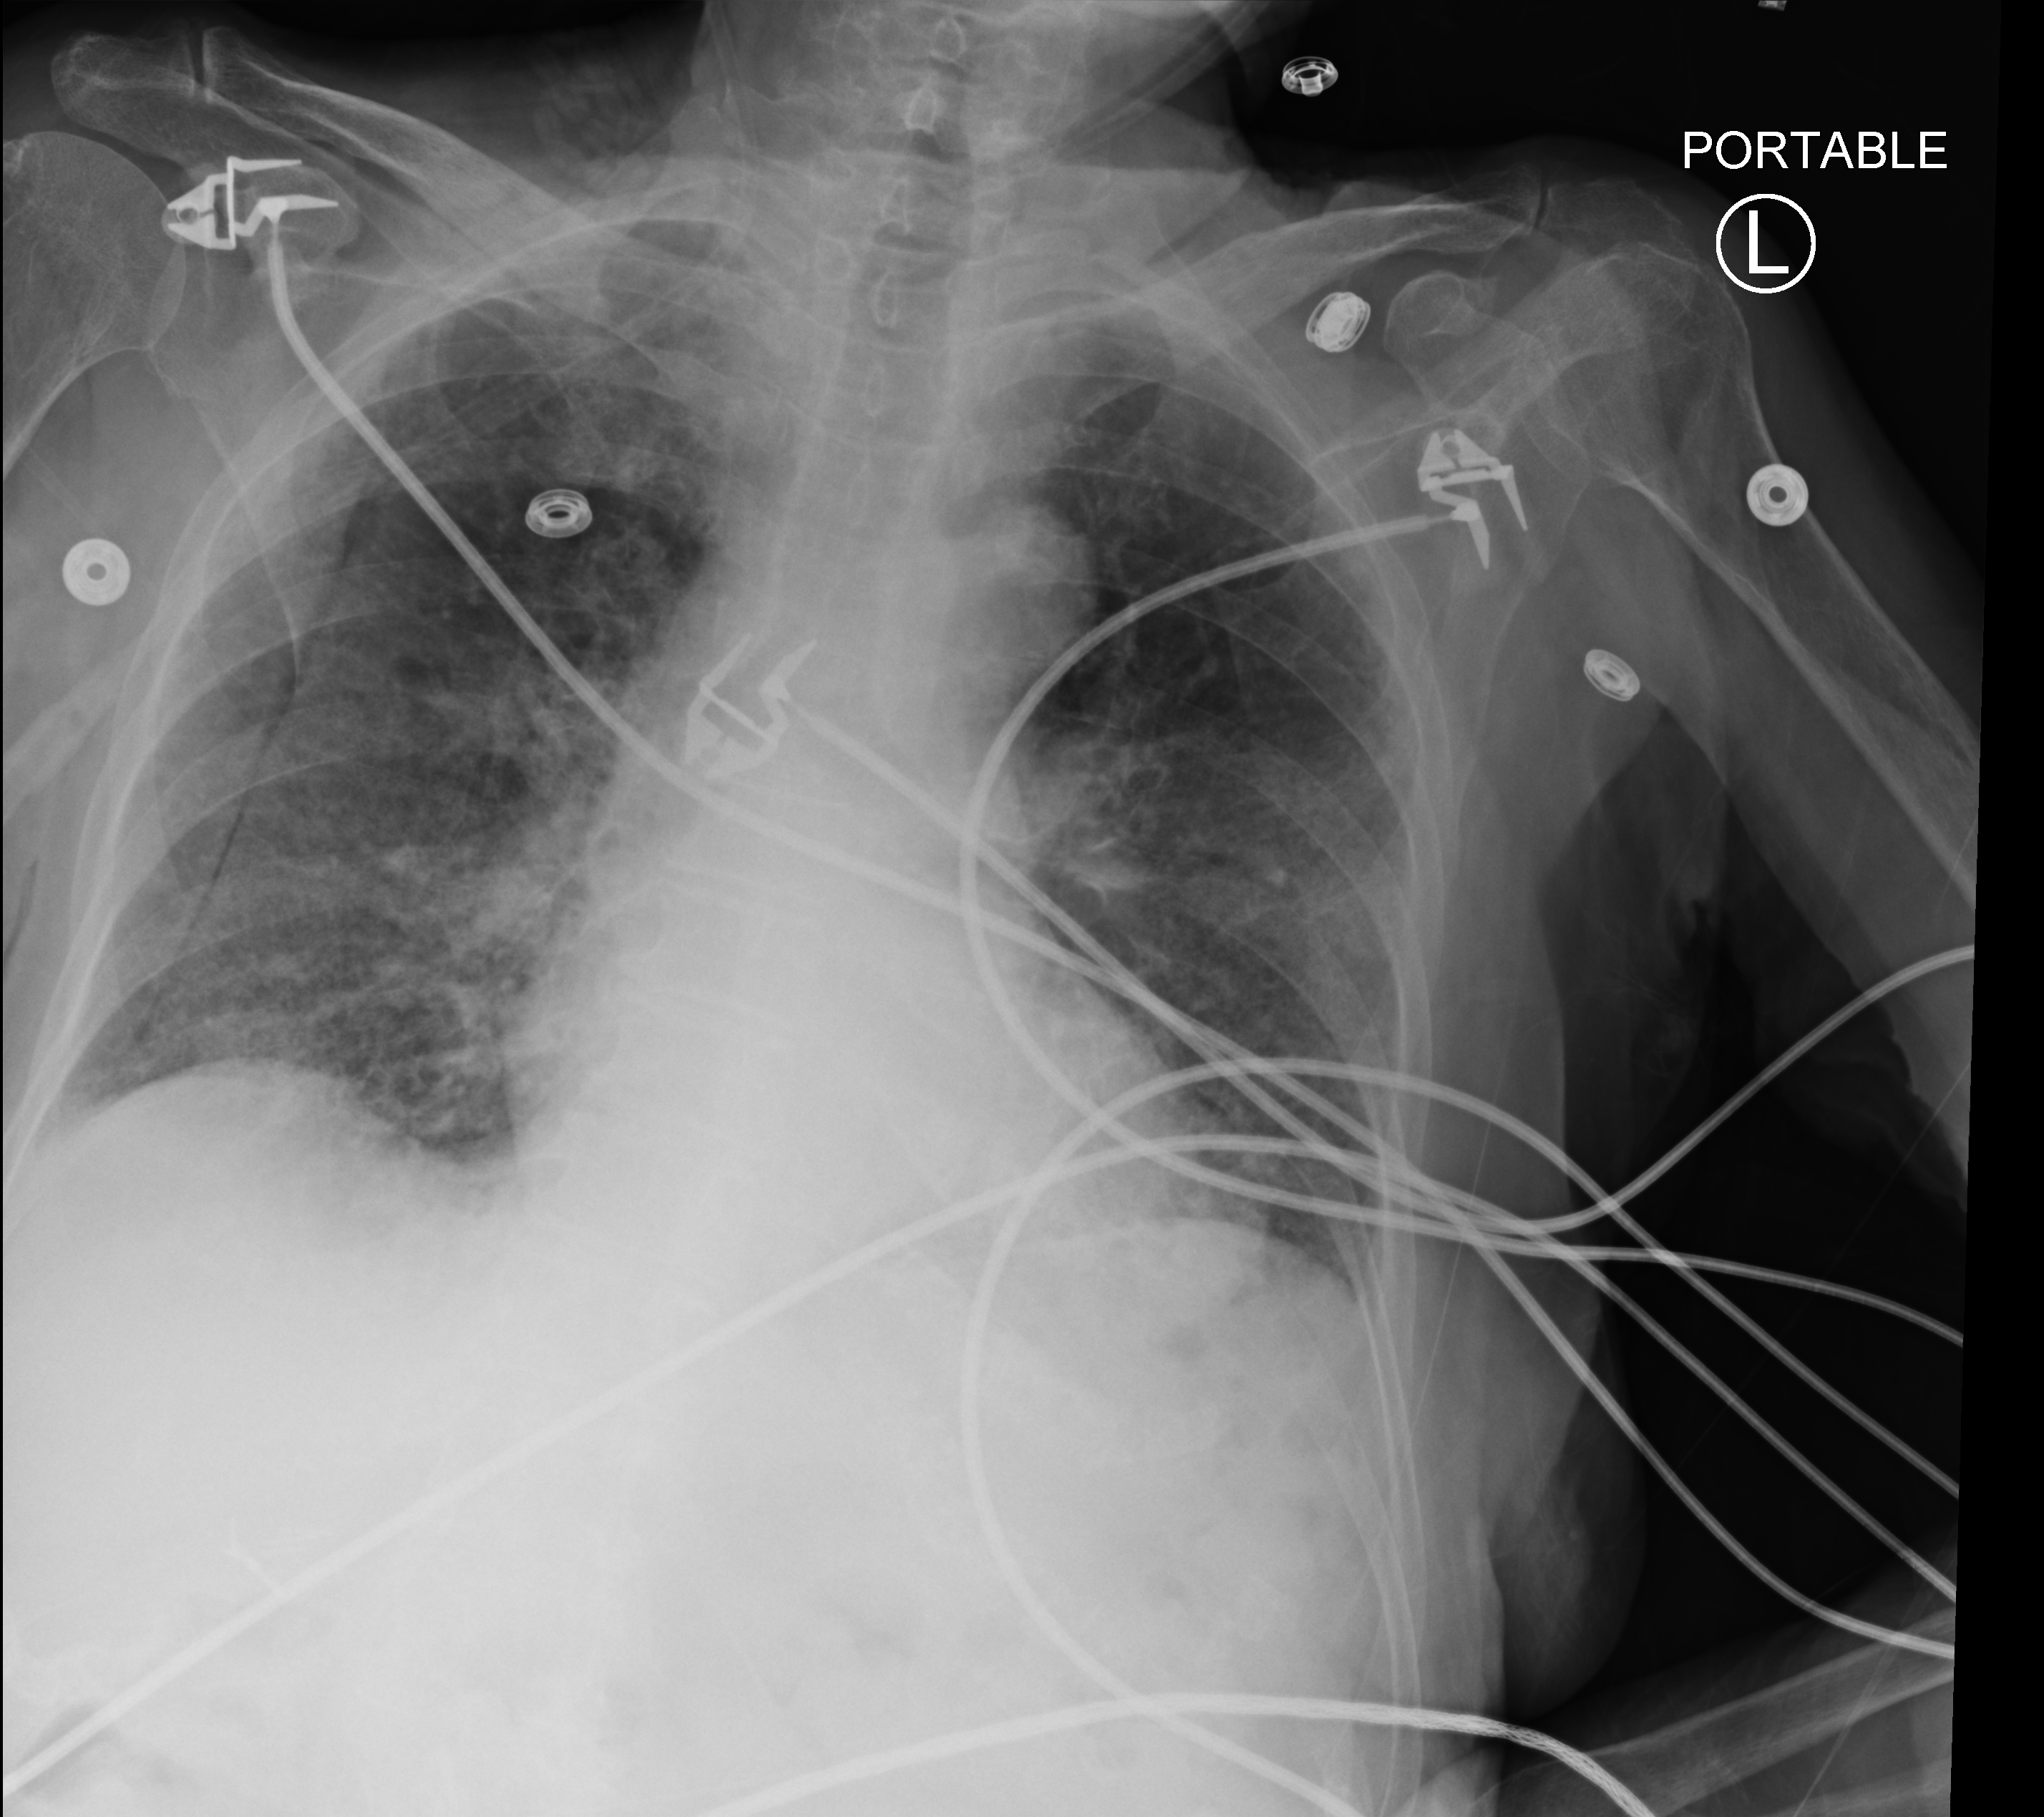
Portable chest radiograph, anteroposterior (AP) projection. Patient hospitalised with COVID-19; female, aged 75–90 years.
Hospital-stay facts (about this admission, not read from this image; timing relative to this image not recorded):
- admitted to intensive care during this hospital stay: no
- mechanically ventilated during this hospital stay: no